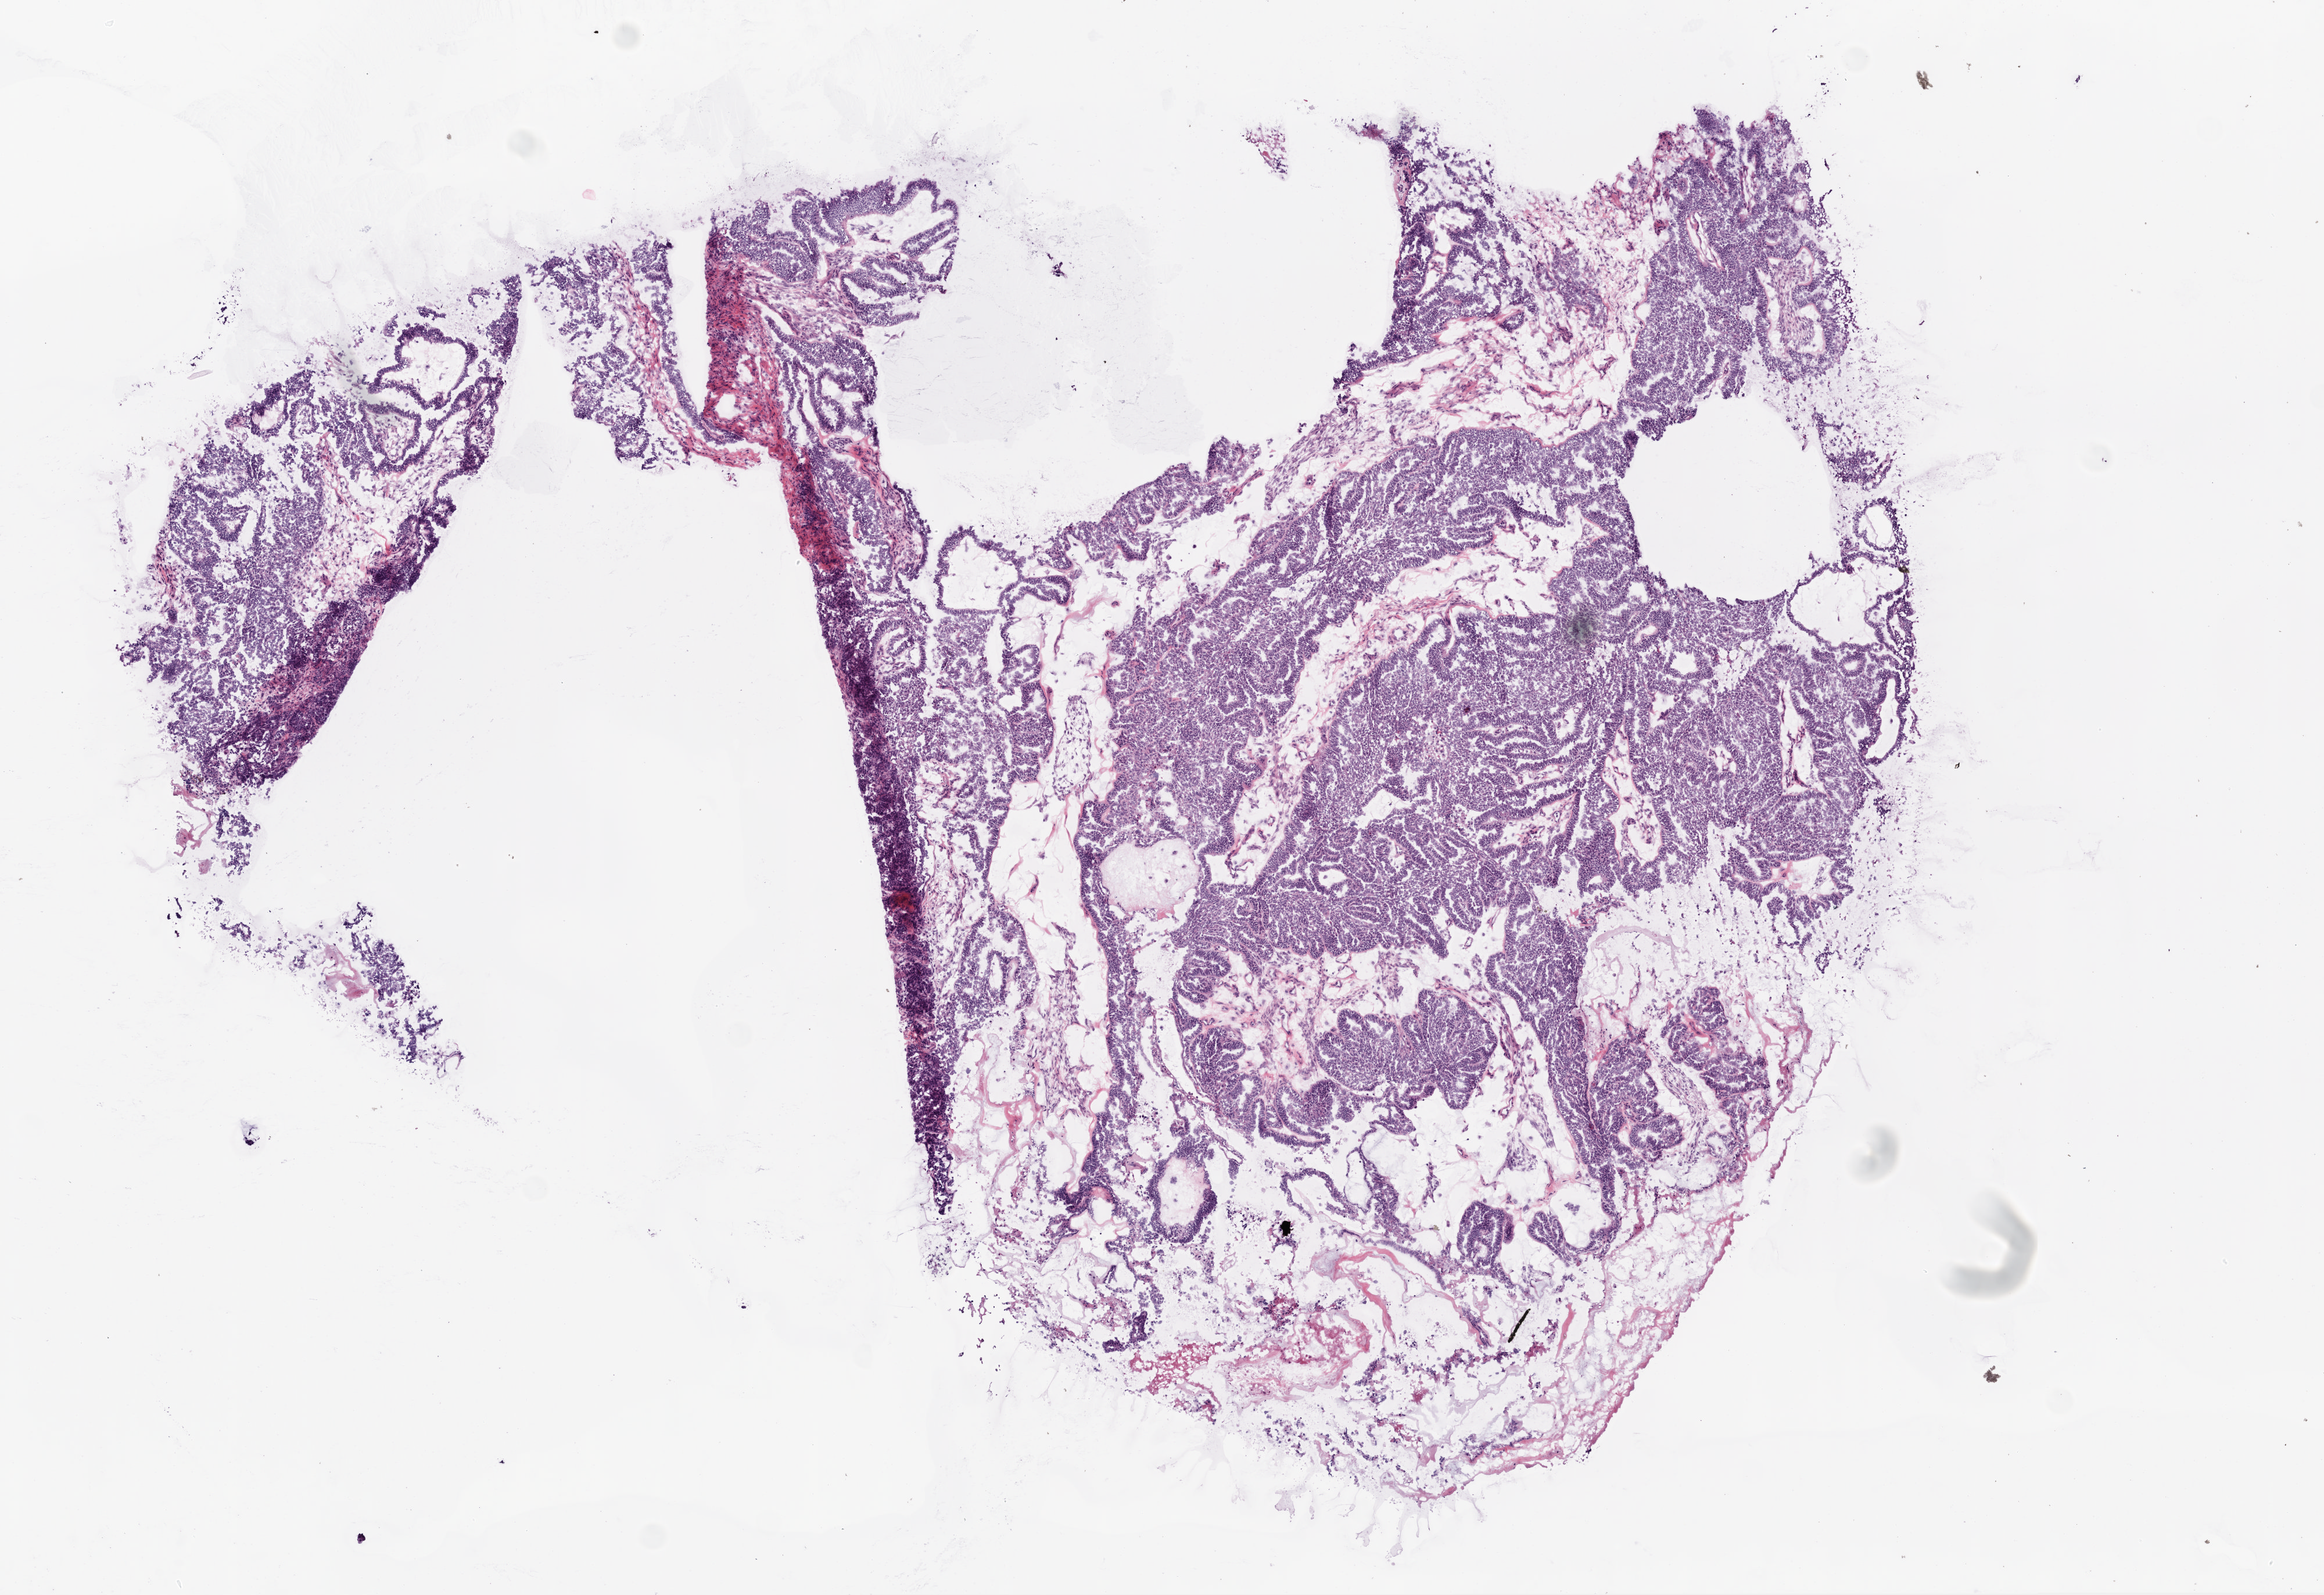
H&E-stained whole-slide image — whole scanned area (about 8.0 x 5.5 mm, slide scanned at 20x) shown as a low-resolution overview, frozen section from the bottom of the tissue portion, ovary, primary tumour sample. Female patient; age at initial diagnosis 65 years. Histologic grade: G2 (moderately differentiated). Composition of this section per pathologist review: tumour cells 60%, tumour nuclei 96%, normal cells 0%, stromal cells 40%, necrosis 0%.
• diagnosis: Serous cystadenocarcinoma, NOS
• FIGO stage: IIA